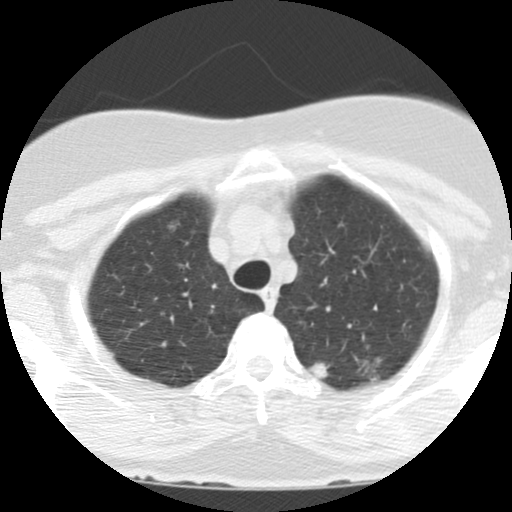
Axial slice from a low-dose chest CT screening exam, first (baseline) screen, lung window (W 1500 / L -600 HU), standard (soft-tissue) reconstruction kernel (STANDARD), 120 kVp, slice 19 of 123 in the series, 512 × 512 image matrix, field of view 290 × 290 mm. Female participant, aged 60 years at enrolment.
• Expert reader's lesion annotation, bounding box (x1, y1, x2, y2) in pixels: (303, 357, 338, 385).
• The screening reader recorded 3 non-calcified nodules or masses ≥4 mm on this exam (left upper lobe, right upper lobe, right upper lobe); which of them this box marks is not recorded.
• Official screen result: positive, change unspecified: nodule(s) >= 4 mm or enlarging nodule(s), mass(es), or other non-specific abnormalities suspicious for lung cancer.
• Later outcome: lung cancer diagnosed 31 days after this screen — bronchiolo-alveolar adenocarcinoma, NOS, left upper lobe, moderately differentiated (G2), stage IA (AJCC 6th edition), 15 mm at pathology.